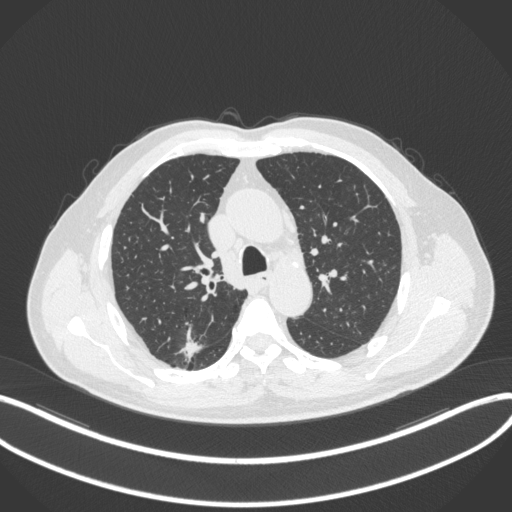
Chest CT, one axial slice; position 257 of 366 along the scan axis; lung window (W 1500 / L -600 HU); 1 mm slice thickness; 512 × 512 image matrix, field of view 400 × 400 mm. Male patient, age 69 years. From the clinical record (not read from this slice): clinical TNM (as recorded): T1b N0 M0; histopathological grade: G2-3.
Annotated regions visible in this slice (rectangle marked by the reading radiologist):
- lung tumour (recorded histology: adenocarcinoma): box from (x=174, y=328) to (x=206, y=362) px